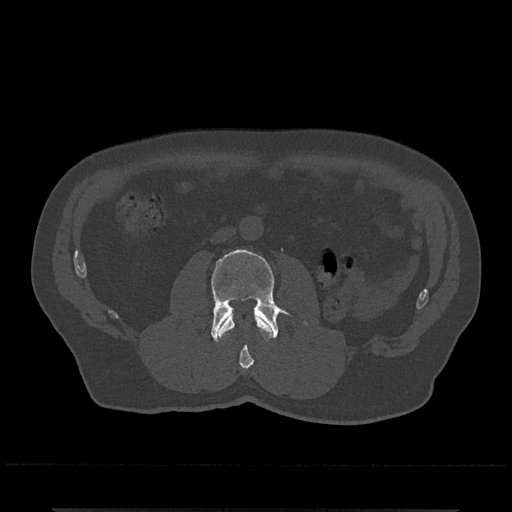
CT including the spine, one axial slice. Position 243 of 797 along the scan axis. Reconstruction kernel Br40s/3. 120 kVp. Bone window (W 1800 / L 400 HU). 0.5 mm slice thickness. 512 × 512 image matrix. Male patient, age 67 years. Case-level facts recorded for this patient, not image findings: primary cancer: prostate.
Outlined on this slice (semi-automatically segmented with operator editing):
- L2 vertebra: bounding box [x1, y1, x2, y2] px = [219, 315, 272, 369]
- L3 vertebra: [211, 249, 289, 342]